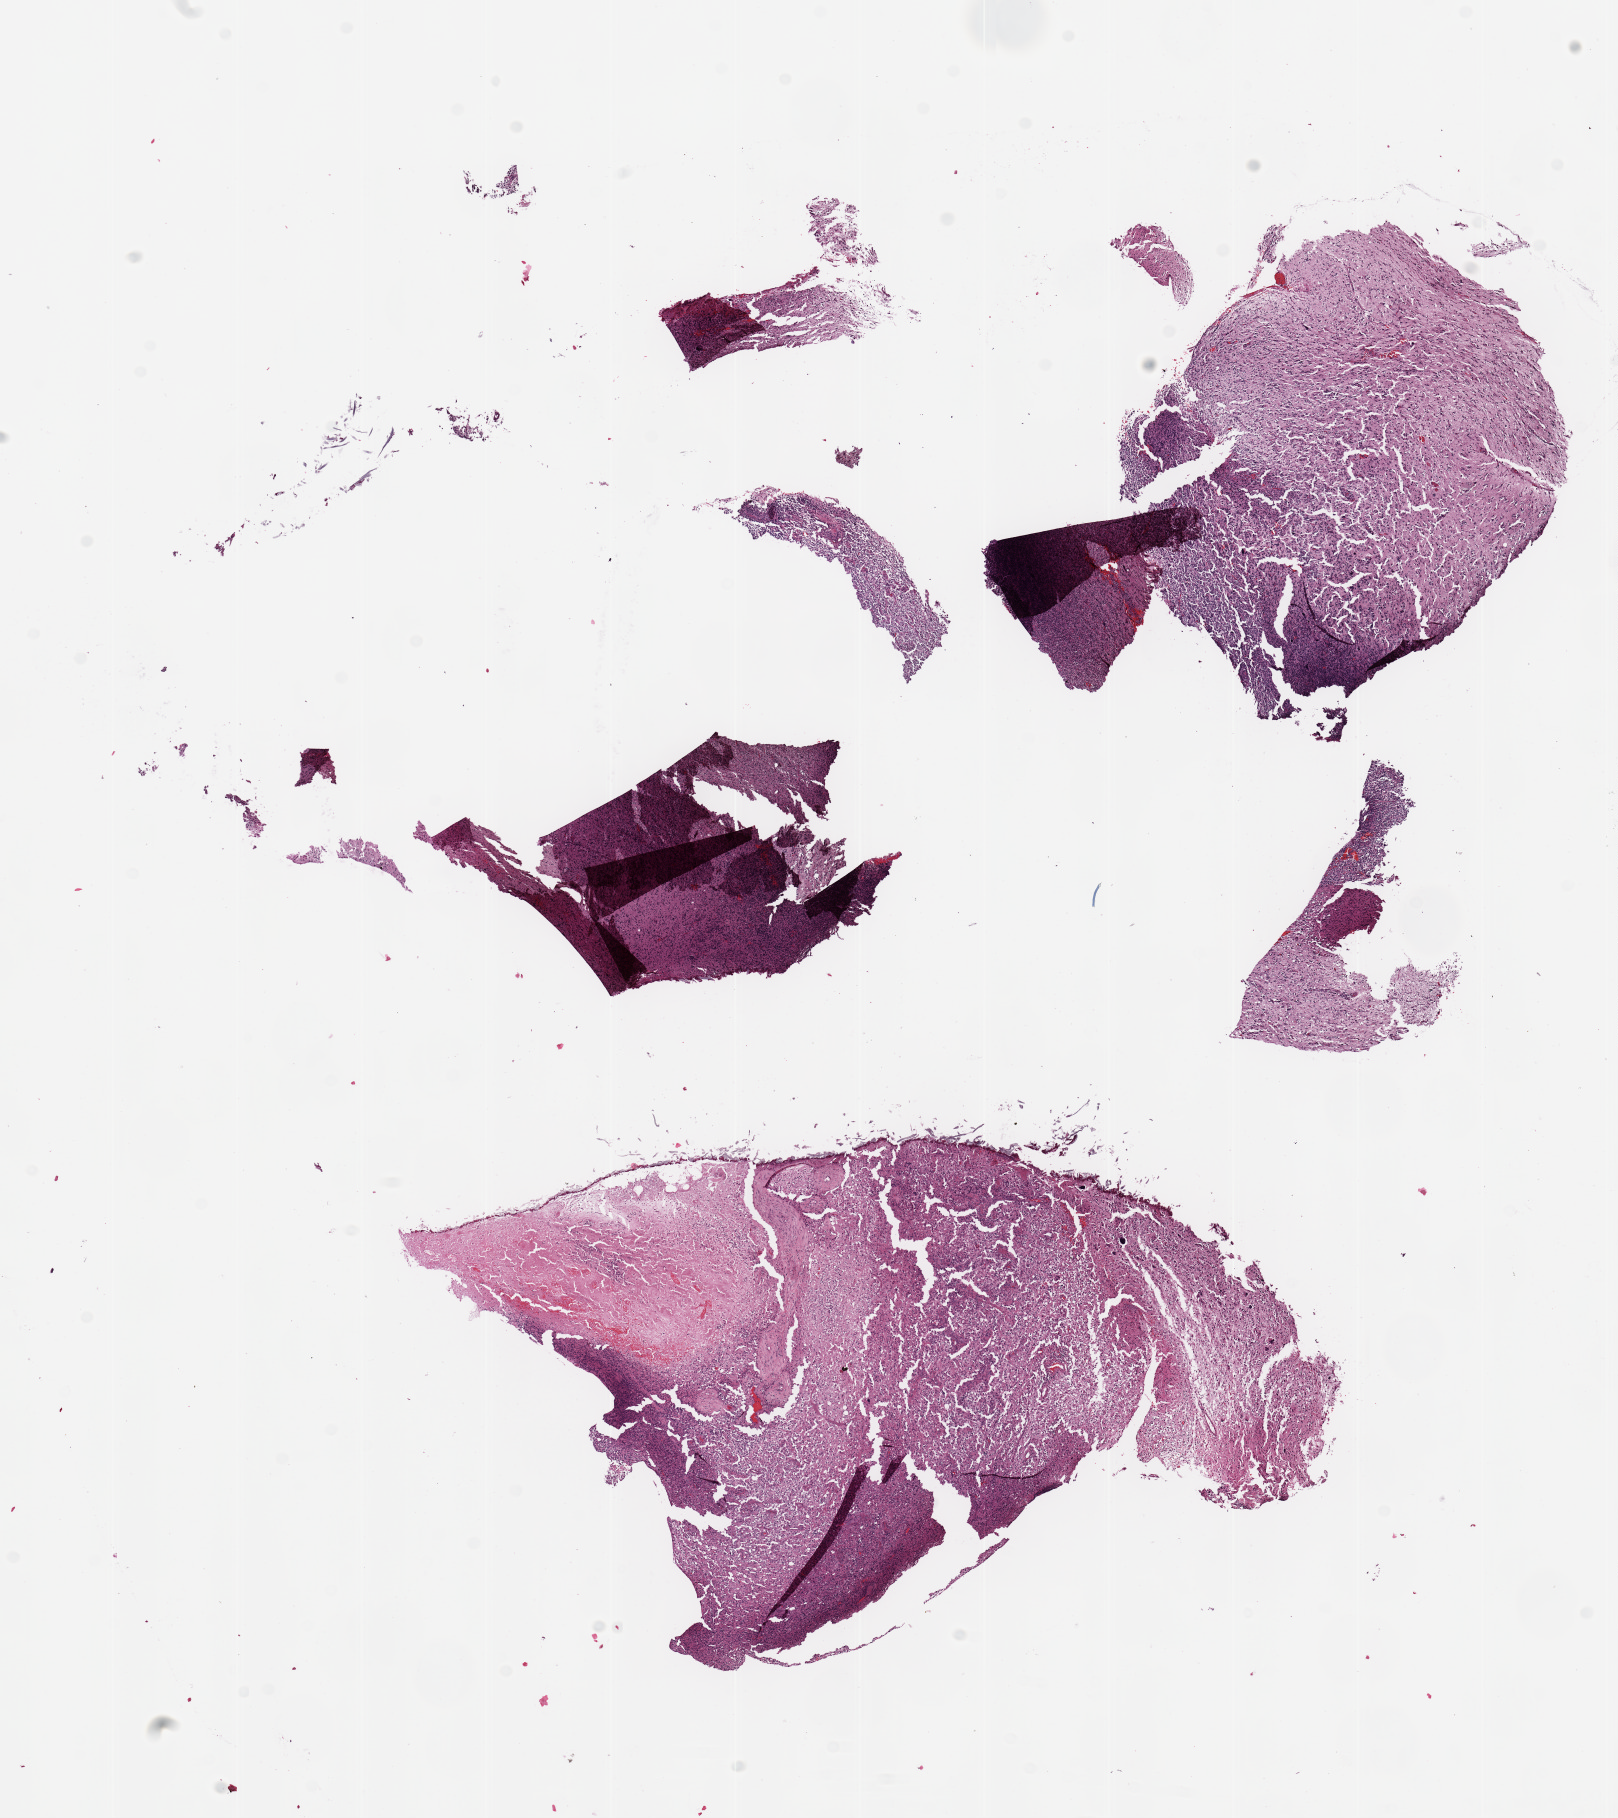
Digitized H&E-stained tissue section (whole slide) — low-resolution overview of the scanned area, about 12.8 x 14.4 mm (from a 20x scan), tumour tissue sample, brain. 59-year-old male patient.
- histologic diagnosis: Glioblastoma